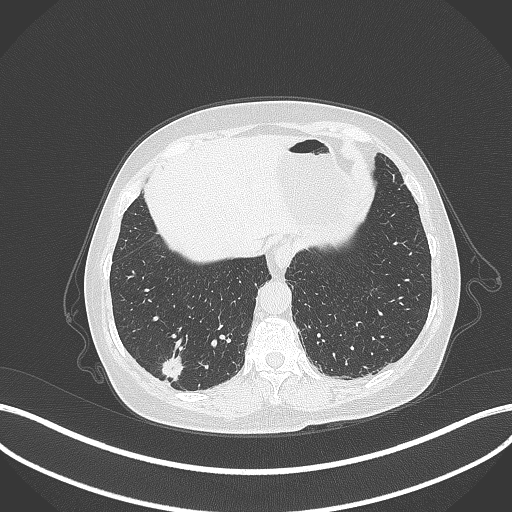
Chest CT, one axial slice; position 58 of 333 along the scan axis; reconstruction kernel B70f; 120 kVp; lung window (W 1500 / L -600 HU); 512 × 512 image matrix, field of view 400 × 400 mm. Female patient, age 69 years. From the clinical record (not read from this slice): clinical TNM (as recorded): T1b N0 M0.
Annotated regions visible in this slice (rectangle marked by the reading radiologist):
- lung tumour (recorded histology: adenocarcinoma): bounding box [x1, y1, x2, y2] px = [158, 351, 183, 382]